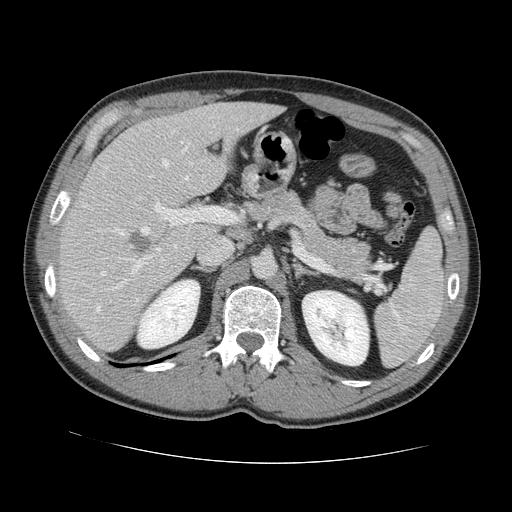
Contrast-enhanced abdominal CT, one axial slice. Position 81 of 131 along the scan axis. 120 kVp. Intravenous contrast given. Soft-tissue window (W 400 / L 40 HU). 2.5 mm slice thickness. 512 × 512 image matrix, field of view 380 × 380 mm. Male patient, age 40 years. Case-level facts recorded for this patient, not image findings: diagnosis: colorectal cancer liver metastases, imaged before liver resection; multiple liver metastases: yes; largest metastasis: 2.9 cm; disease in both lobes: yes.
Annotated regions visible in this slice (expert manual segmentation):
- hepatic veins: bounding box (x1, y1, x2, y2) in pixels: (96, 142, 190, 311)
- liver: (61, 103, 279, 350)
- planned liver remnant (the part of the liver to remain after resection): (104, 102, 279, 199)
- portal vein (with intrahepatic branches): (106, 197, 233, 291)
- liver metastasis: (130, 231, 156, 256)